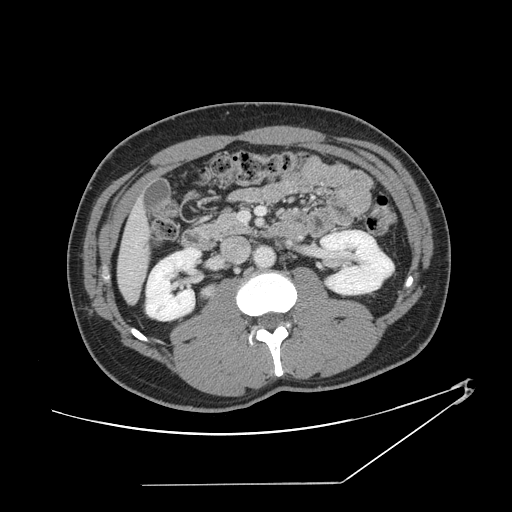
Contrast-enhanced abdominal CT, one axial slice. Position 52 of 152 along the scan axis. Reconstruction kernel STANDARD. 120 kVp. Intravenous contrast given. Soft-tissue window (W 400 / L 40 HU). 512 × 512 image matrix, field of view 432 × 432 mm. Male patient, age 45 years. From the clinical record (not read from this slice): diagnosis: colorectal cancer liver metastases, imaged before liver resection; multiple liver metastases: no; largest metastasis: 1 cm; disease in both lobes: no.
Structures marked on this image (outlined manually by an expert reader):
- hepatic veins: bounding box (x1, y1, x2, y2) in pixels: (135, 240, 140, 248)
- liver: (118, 206, 148, 302)
- planned liver remnant (the part of the liver to remain after resection): (118, 206, 148, 302)
- portal vein (with intrahepatic branches): (241, 207, 265, 222)